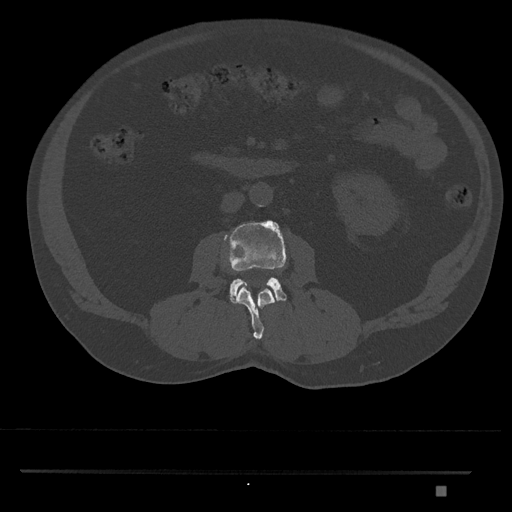
CT including the spine, one axial slice; position 716 of 1134 along the scan axis; reconstruction kernel Br40s/3; 120 kVp; bone window (W 1800 / L 400 HU); 0.5 mm slice thickness; 512 × 512 image matrix, field of view 429 × 429 mm. Male patient, age 65 years. From the clinical record (not read from this slice): primary cancer: prostate.
Structures marked on this image (semi-automatically segmented with operator editing):
- L2 vertebra: bounding box [x1, y1, x2, y2] px = [237, 286, 275, 340]
- L3 vertebra: [224, 220, 287, 304]